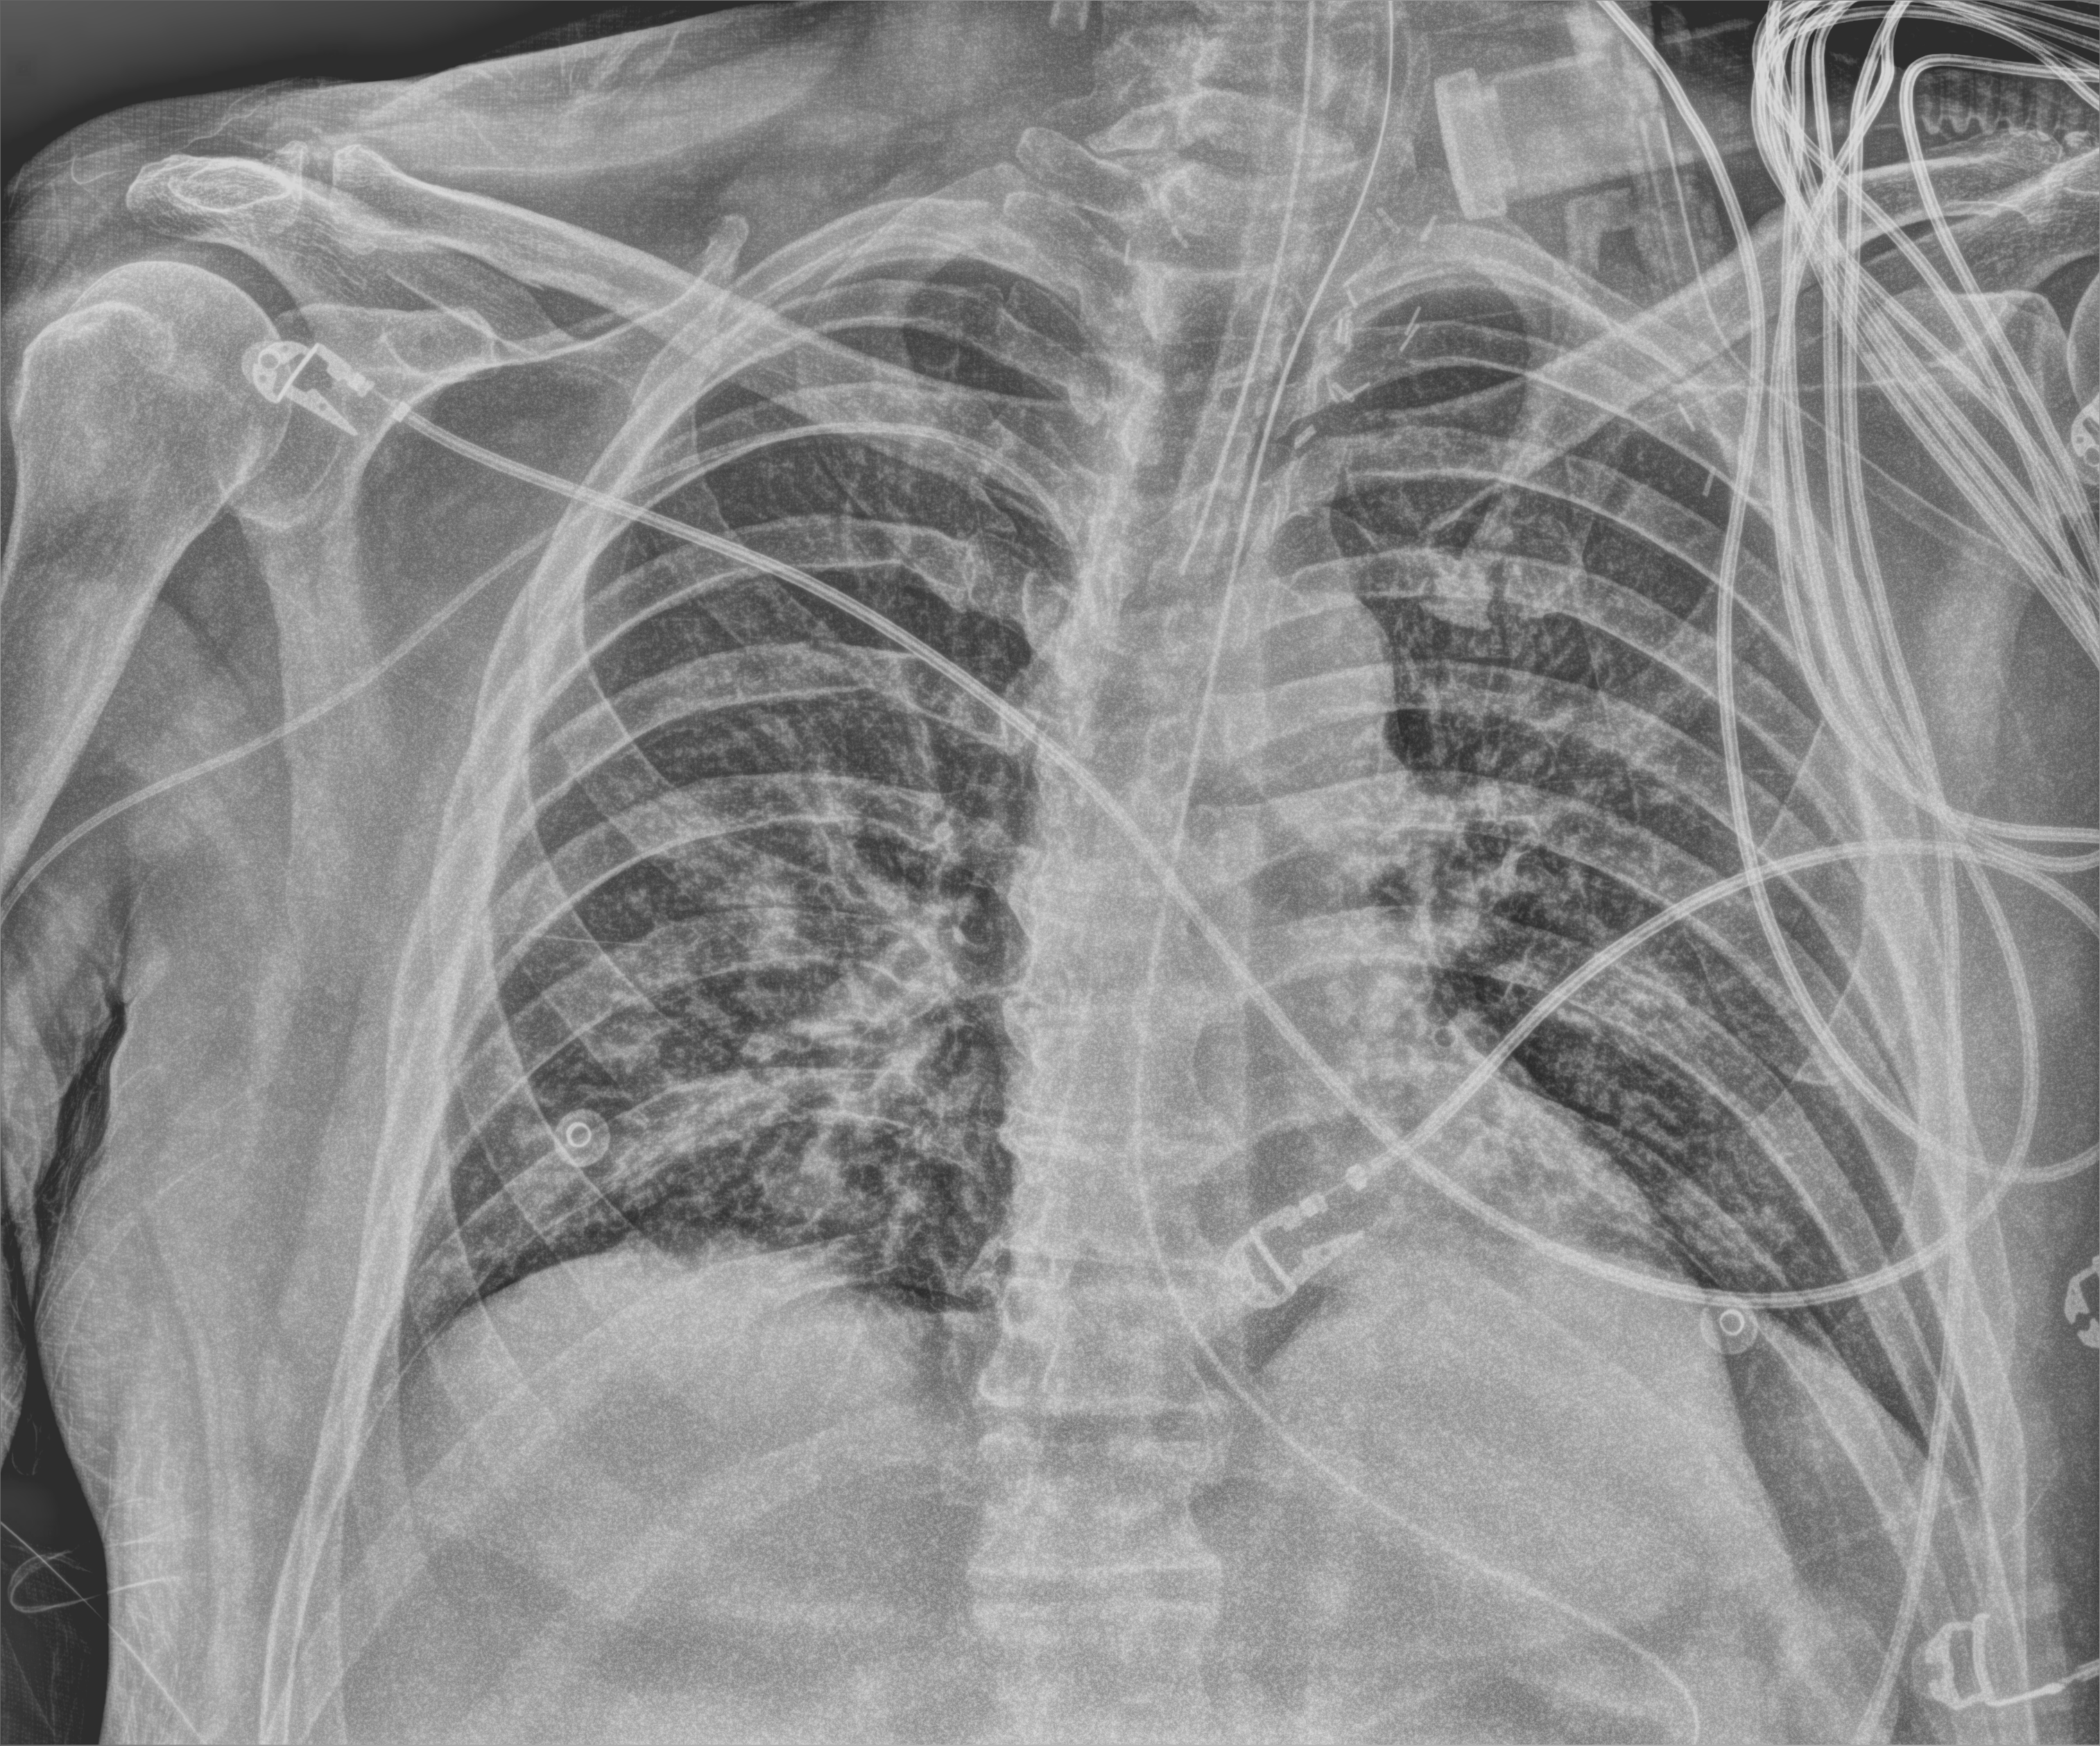
Bedside chest radiograph (computed radiography), anteroposterior (AP) projection. Patient hospitalised with COVID-19, aged 18–59 years.
From the hospital-stay record, not from the radiograph (when in the stay this image was taken is not recorded): admitted to intensive care during this hospital stay: yes; mechanically ventilated during this hospital stay: yes.